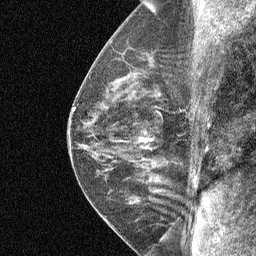
Breast MRI (dynamic contrast-enhanced), one sagittal slice; position 38 of 64 along the scan axis; dynamic contrast-enhanced study with each time point stored as its own series, time point 2 of 4 at this slice position (early post-contrast, ordered by acquisition time); 1.5 T; TE 4.8 ms, TR 27 ms; 256 × 256 image matrix, field of view 180 × 180 mm. Female patient, age 50 years. From the clinical record (not read from this slice): setting: breast cancer imaged before/during neoadjuvant chemotherapy; receptor status: HER2-positive.
Annotated regions visible in this slice (semi-automatically segmented with operator editing):
- analysis volume of interest (the breast-tissue region the enhancement analysis was run in; not a lesion): bounding box (x1, y1, x2, y2) in pixels: (123, 91, 181, 177)
- tumour enhancement mask (voxels above the 90 % enhancement threshold inside the analysis volume of interest): (140, 138, 148, 141)